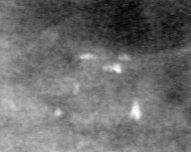
Crop from a digitized film mammogram around one marked abnormality, right breast, CC view, BI-RADS breast density category 4 (scale 1–4).
- Calcifications, morphology pleomorphic, distribution clustered; BI-RADS assessment category 4; subtlety rating 2 on a 1 (subtle) to 5 (obvious) scale; pathology (as recorded): malignant.